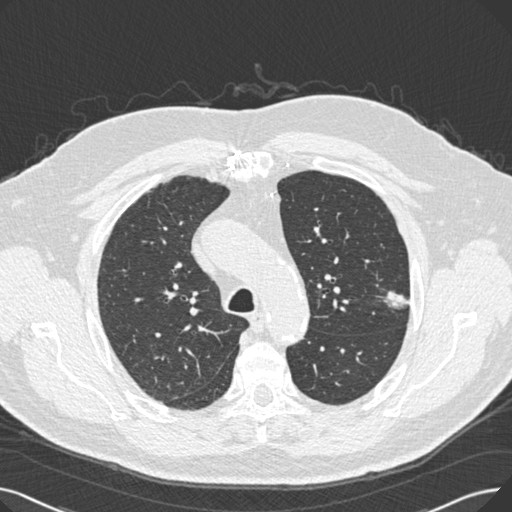
Low-dose screening chest CT, one axial slice; slice 191 of 269 in the series (ordered by position); 120 kVp; lung window (W 1500 / L -600 HU); 1 mm slice thickness; 512 × 512 image matrix, field of view 370 × 370 mm.
Annotated regions visible in this slice (expert manual segmentation):
- lesion 1 (tumor, upper lobe of left lung): bounding box <383,291,409,309> (left, top, right, bottom; pixels)